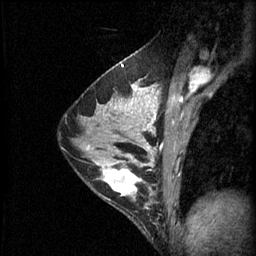
Breast MRI (dynamic contrast-enhanced), one sagittal slice; slice 35 of 60 in the series (ordered by position); 3 images stored at this slice position (order not interpretable as contrast timing); 1.5 T; TE 4.2 ms, TR 11 ms; 2.1 mm slice thickness; 256 × 256 image matrix, field of view 180 × 180 mm. Female patient, age 29 years.
Outlined on this slice (semi-automatic segmentation, software-assisted and operator-edited):
- analysis volume of interest (the breast-tissue region the enhancement analysis was run in; not a lesion): bounding box (x1, y1, x2, y2) in pixels: (96, 164, 153, 221)
- tumour enhancement mask (voxels above the 70 % enhancement threshold inside the analysis volume of interest): (103, 164, 148, 197)